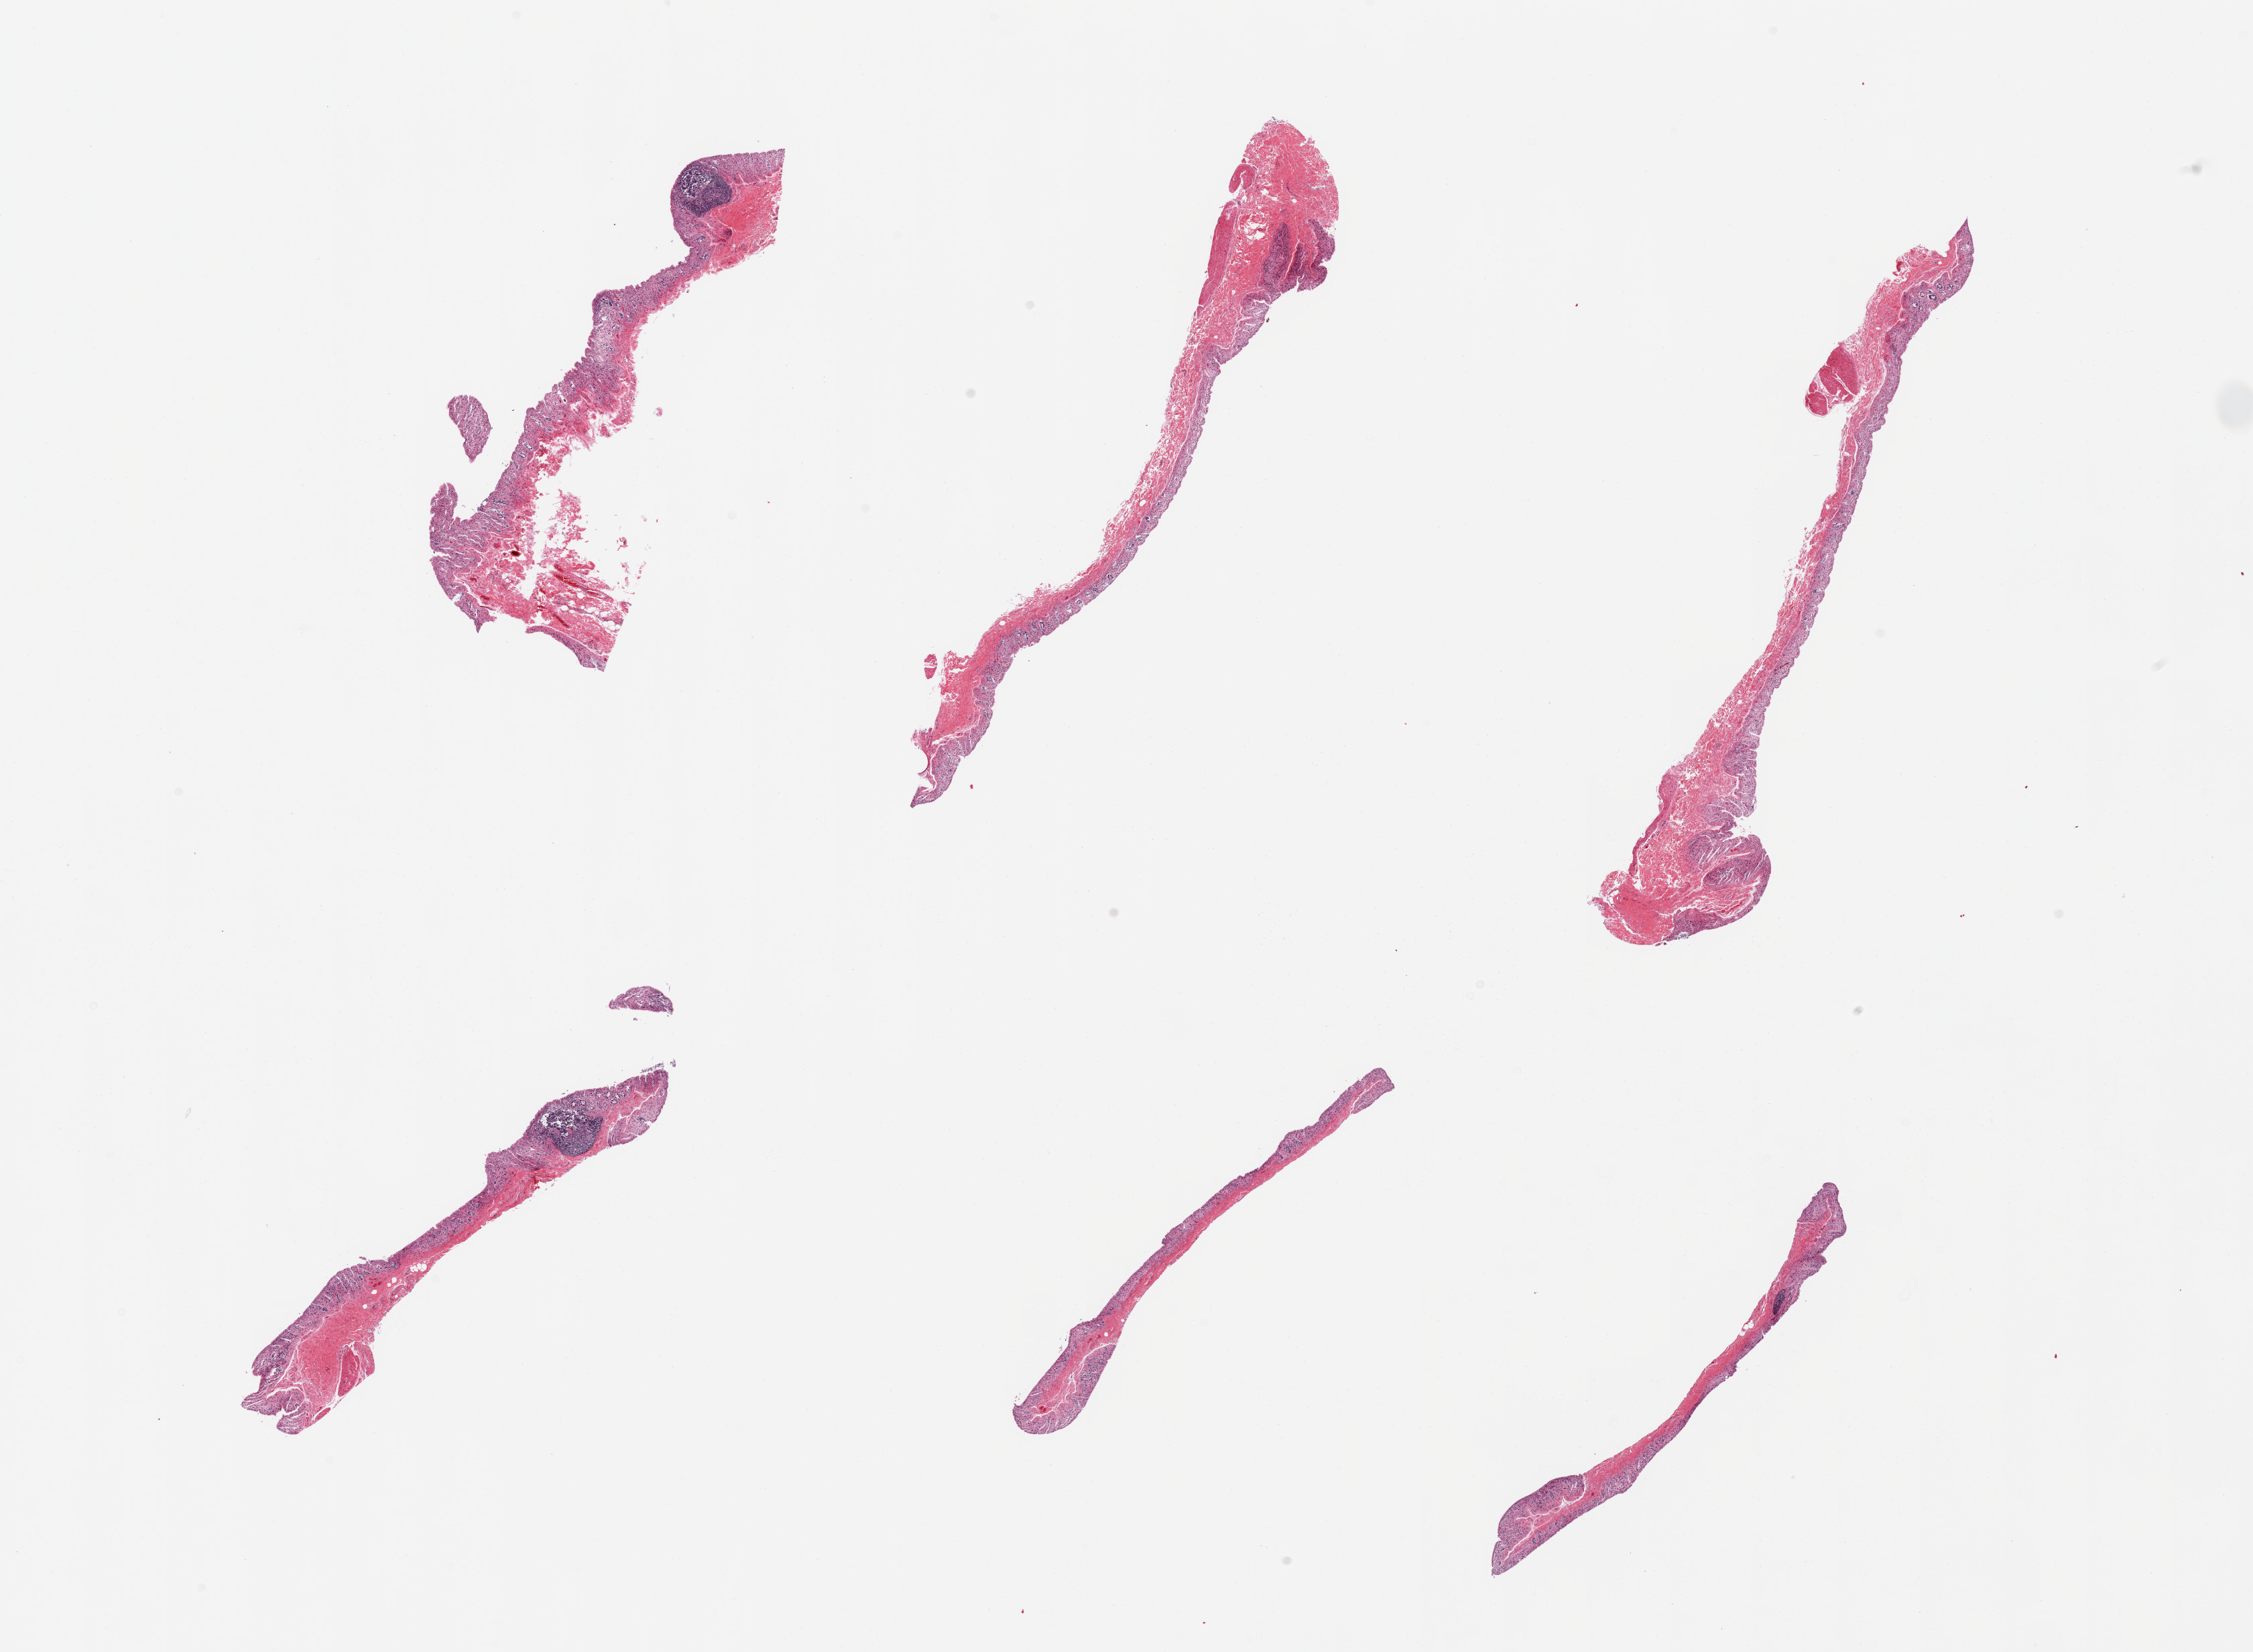
Digitized H&E-stained section — low-resolution overview of the scanned area, about 26.6 x 19.5 mm (acquisition: 20x scan). PAXgene-fixed paraffin-embedded (PFPE) section. Sampled site (target tissue): transverse colon. Tissue donor sample.
Review note (as recorded): 6 pieces; virtually no muscle; mucosa totally autolyzed.